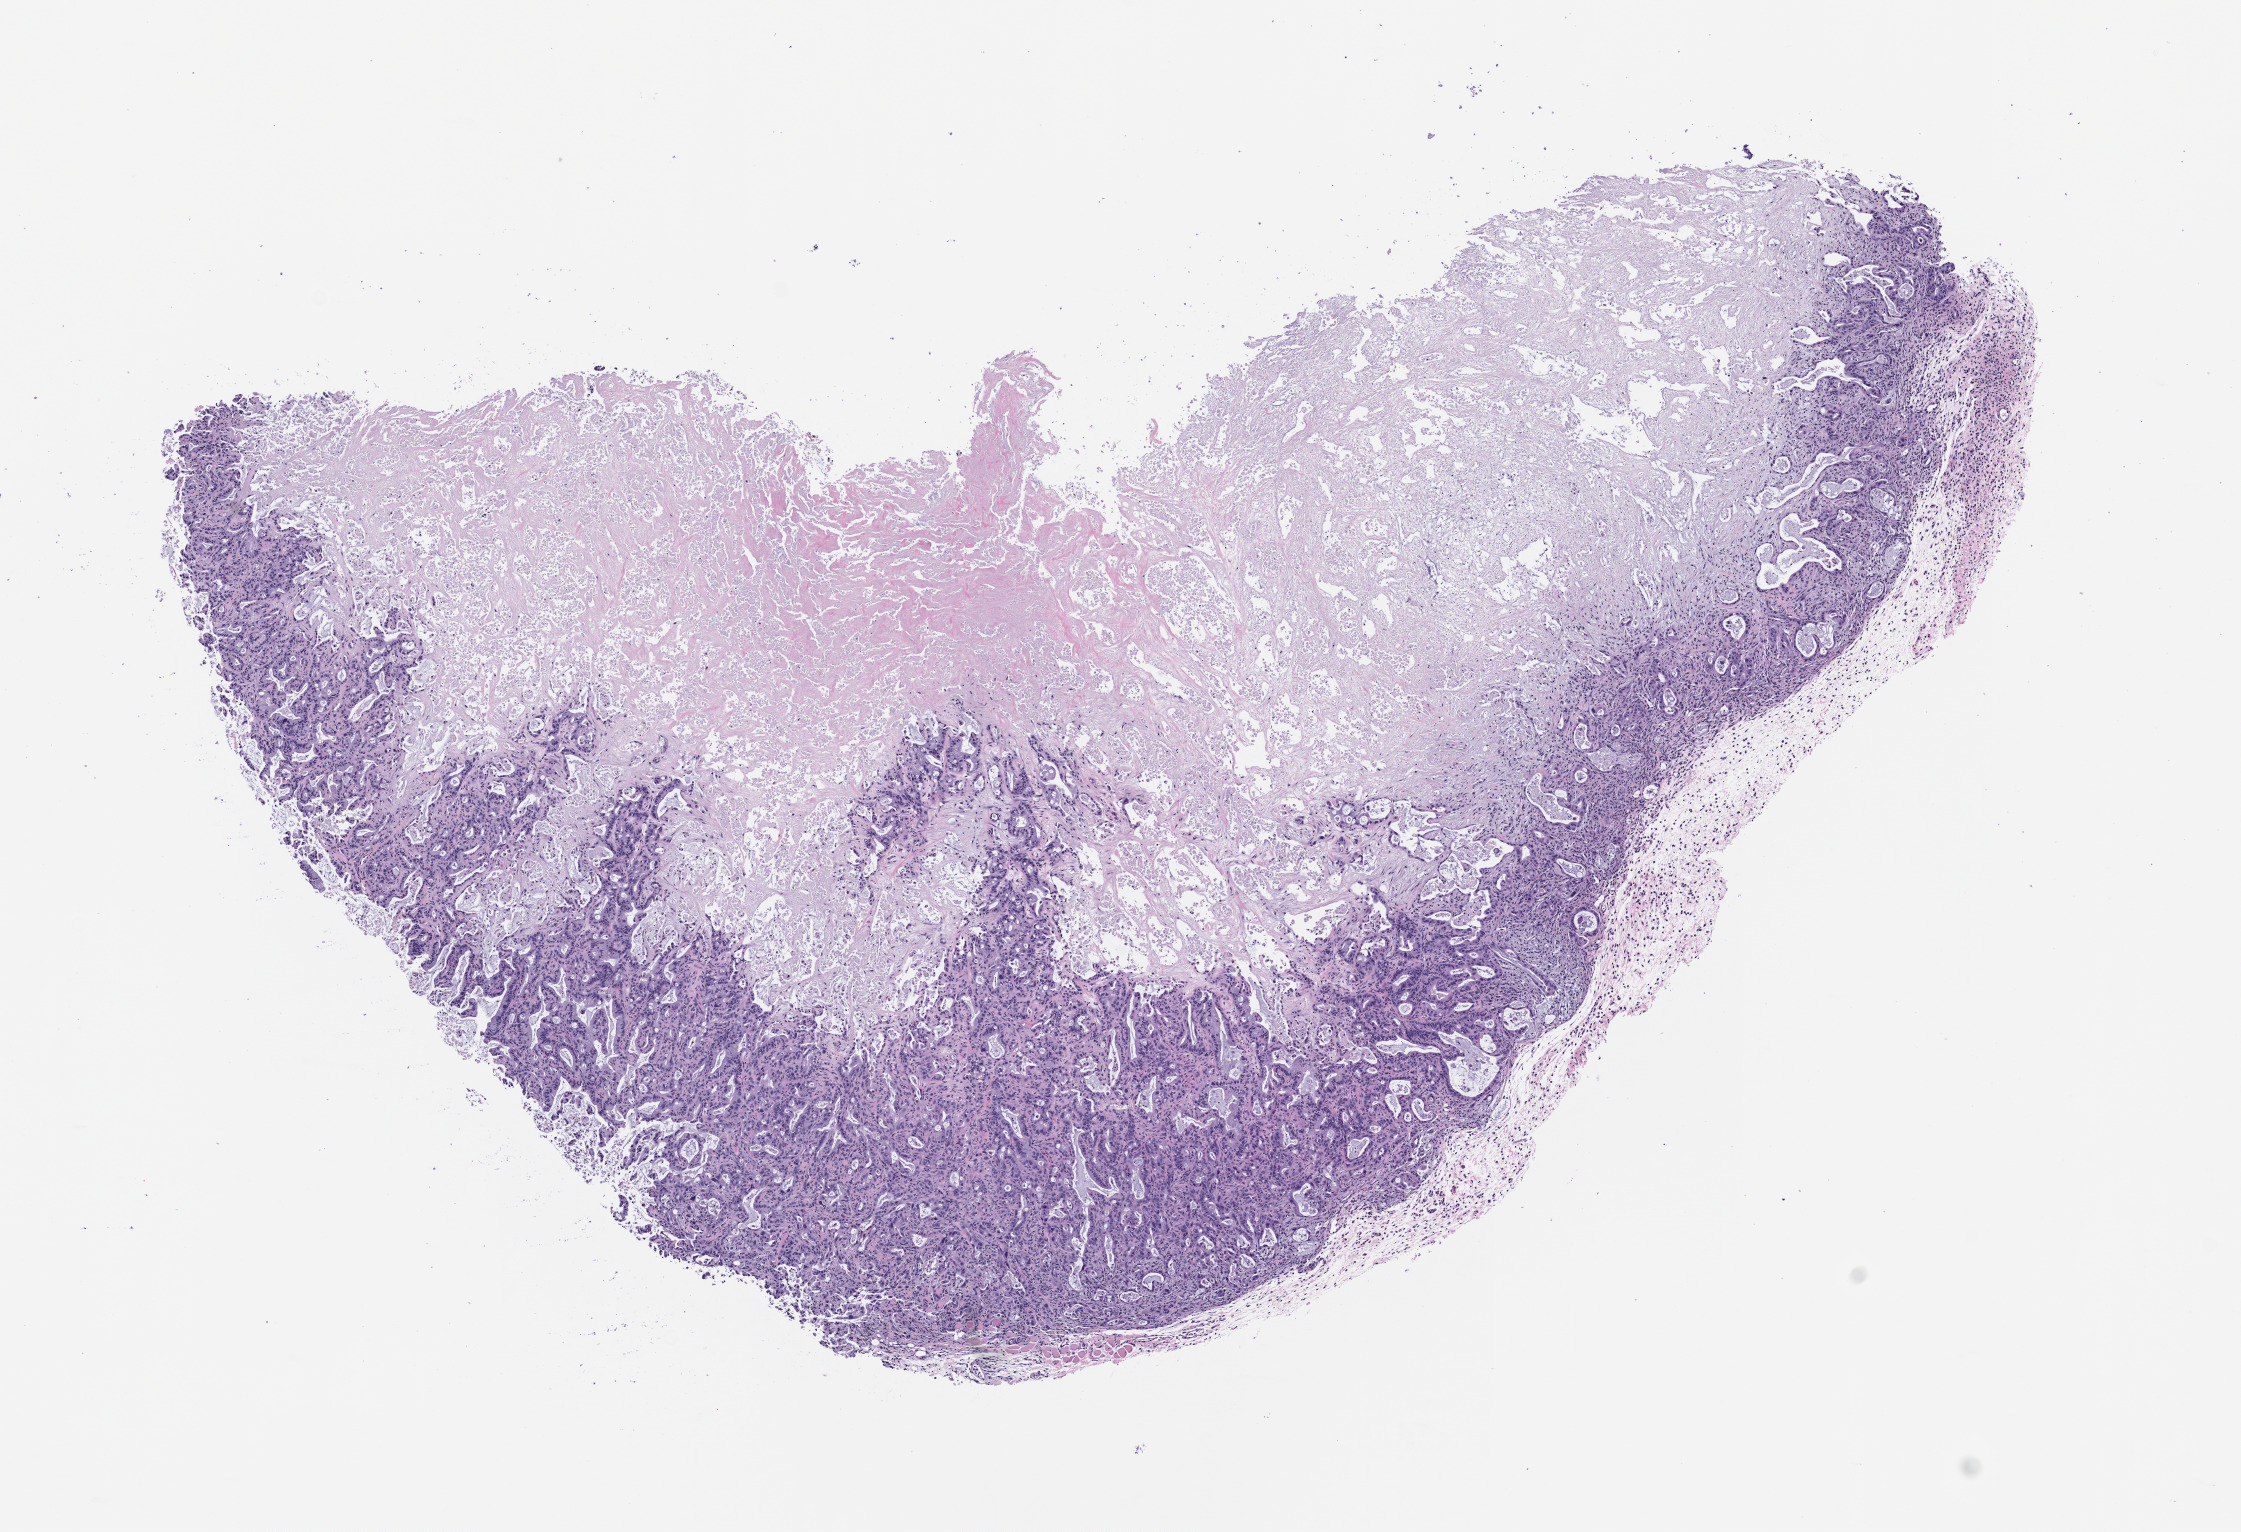
Whole-slide image, hematoxylin and eosin (H&E): patient-derived xenograft (human tumor grown in a mouse), passage 3 — low-resolution overview of the scanned area, about 9.0 x 6.2 mm, FFPE section, originating tumor site category: pancreas.
Originating patient diagnosis: Pancreatic Adenocarcinoma.